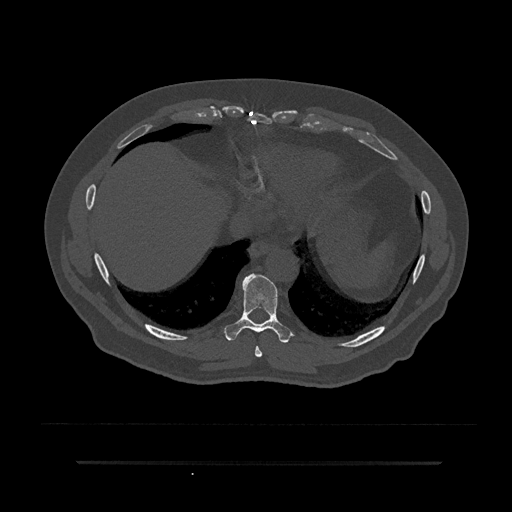
CT including the spine, one axial slice. Slice 381 of 797 in the series (ordered by position). Reconstruction kernel Br40s/3. 120 kVp. Bone window (W 1800 / L 400 HU). 0.5 mm slice thickness. 512 × 512 image matrix, field of view 464 × 464 mm. Patient: male, 59 years. From the clinical record (not read from this slice): primary cancer: bile ducts.
Outlined on this slice (semi-automatic segmentation, software-assisted and operator-edited):
- T8 vertebra: bounding box <255,346,262,358> (left, top, right, bottom; pixels)
- T9 vertebra: <224,273,293,343>